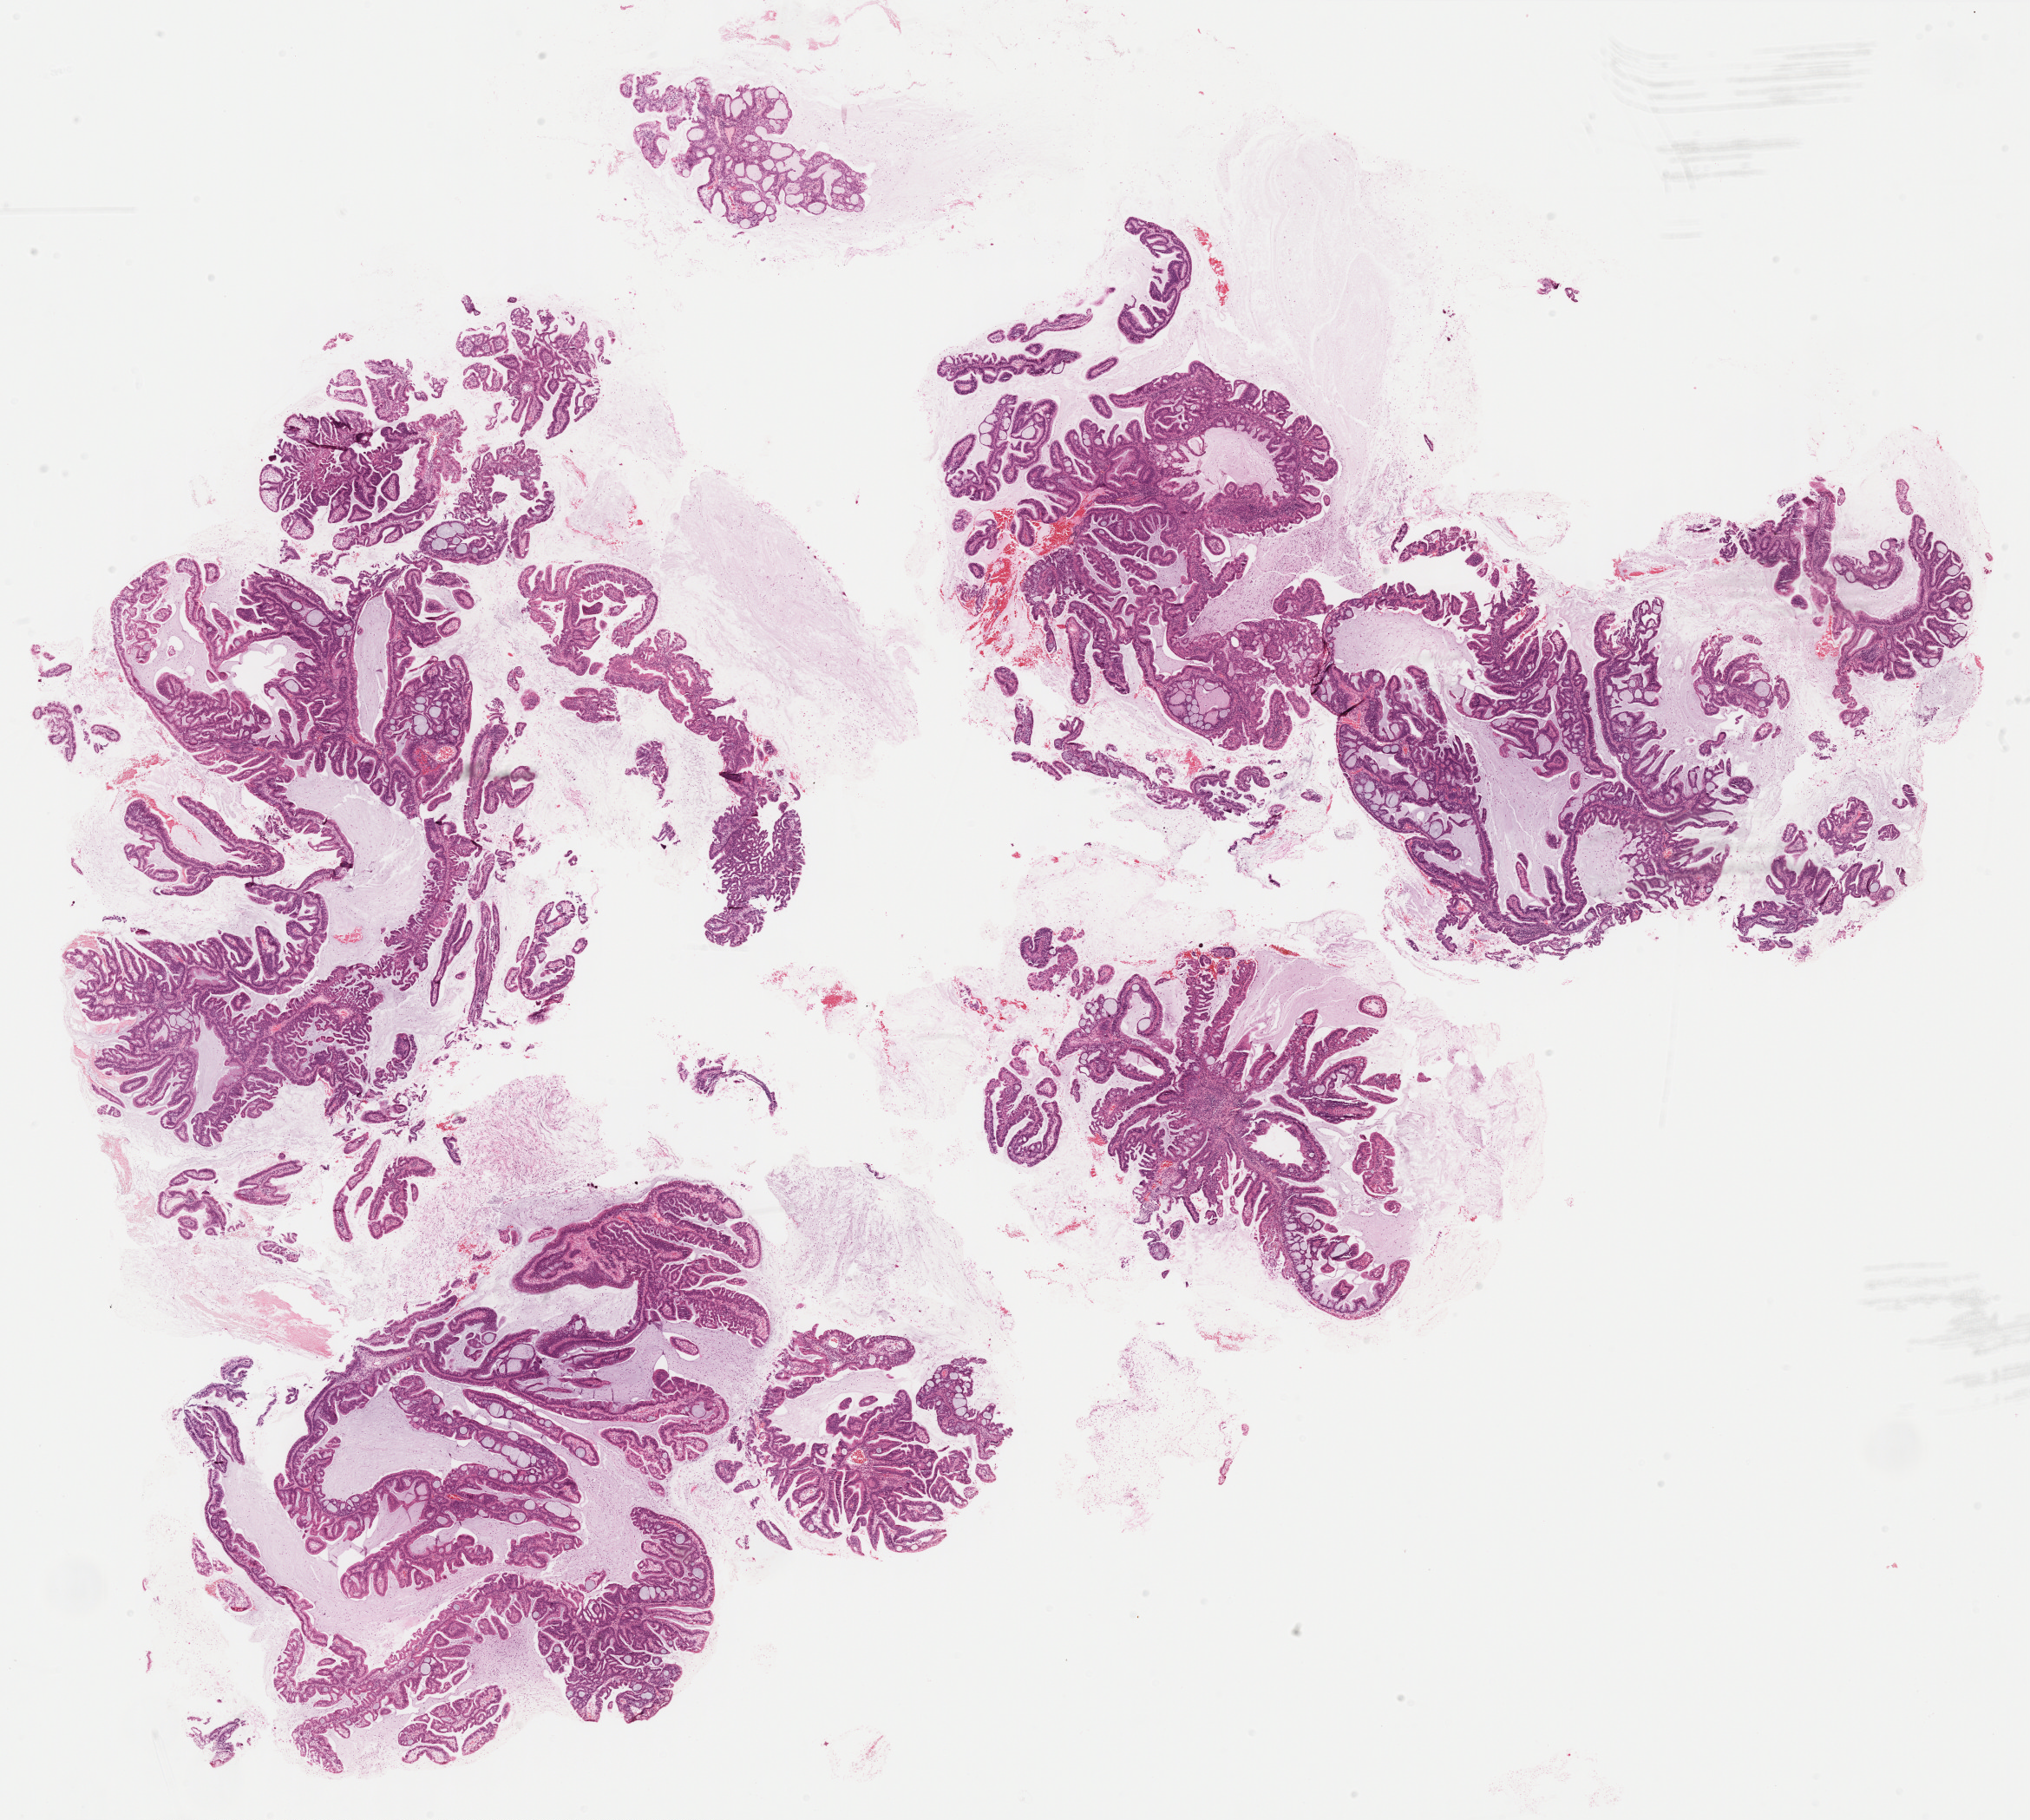
Whole-slide histology image, H&E-stained, shown as a low-resolution overview of the whole scanned area (about 18.7 x 16.8 mm, from a 40x scan); FFPE section; sample: primary tumour, cervix. Female patient; age at initial diagnosis 40 years.
Diagnosis: Adenocarcinoma, NOS.